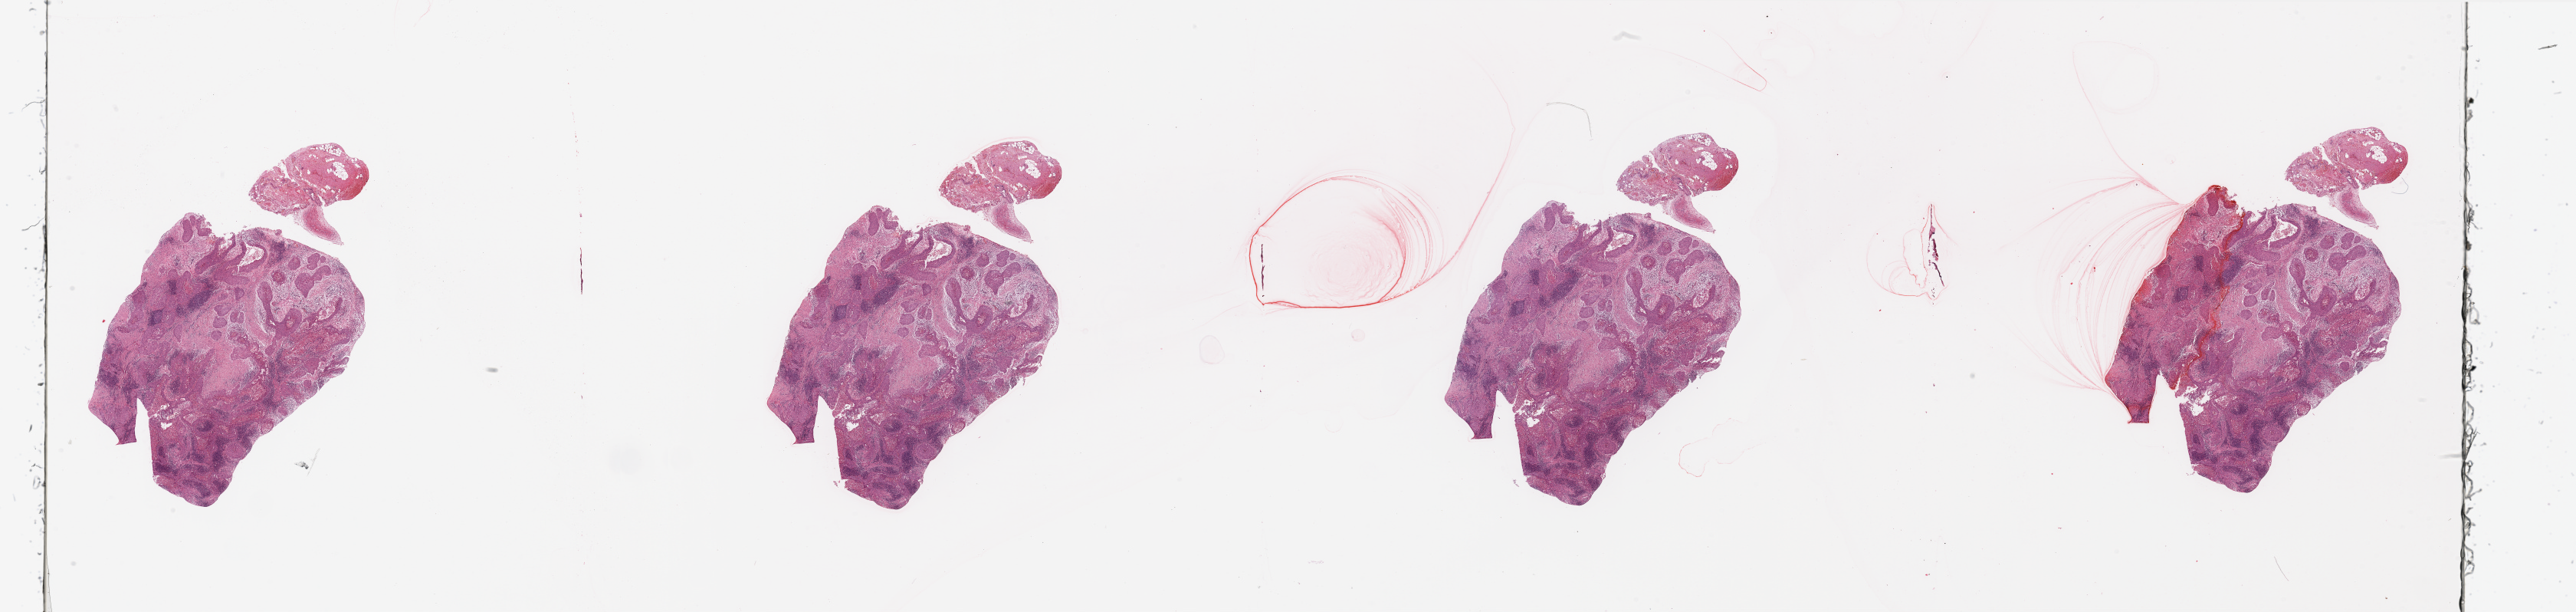
Whole-slide histology image, H&E, shown as a low-resolution overview of the whole scanned area (about 53.2 x 12.6 mm, slide scanned at 20x). Head and neck, tissue type not recorded. Patient: male, age 68 years.
Patient diagnosis: Squamous cell carcinoma, NOS (larynx, NOS).